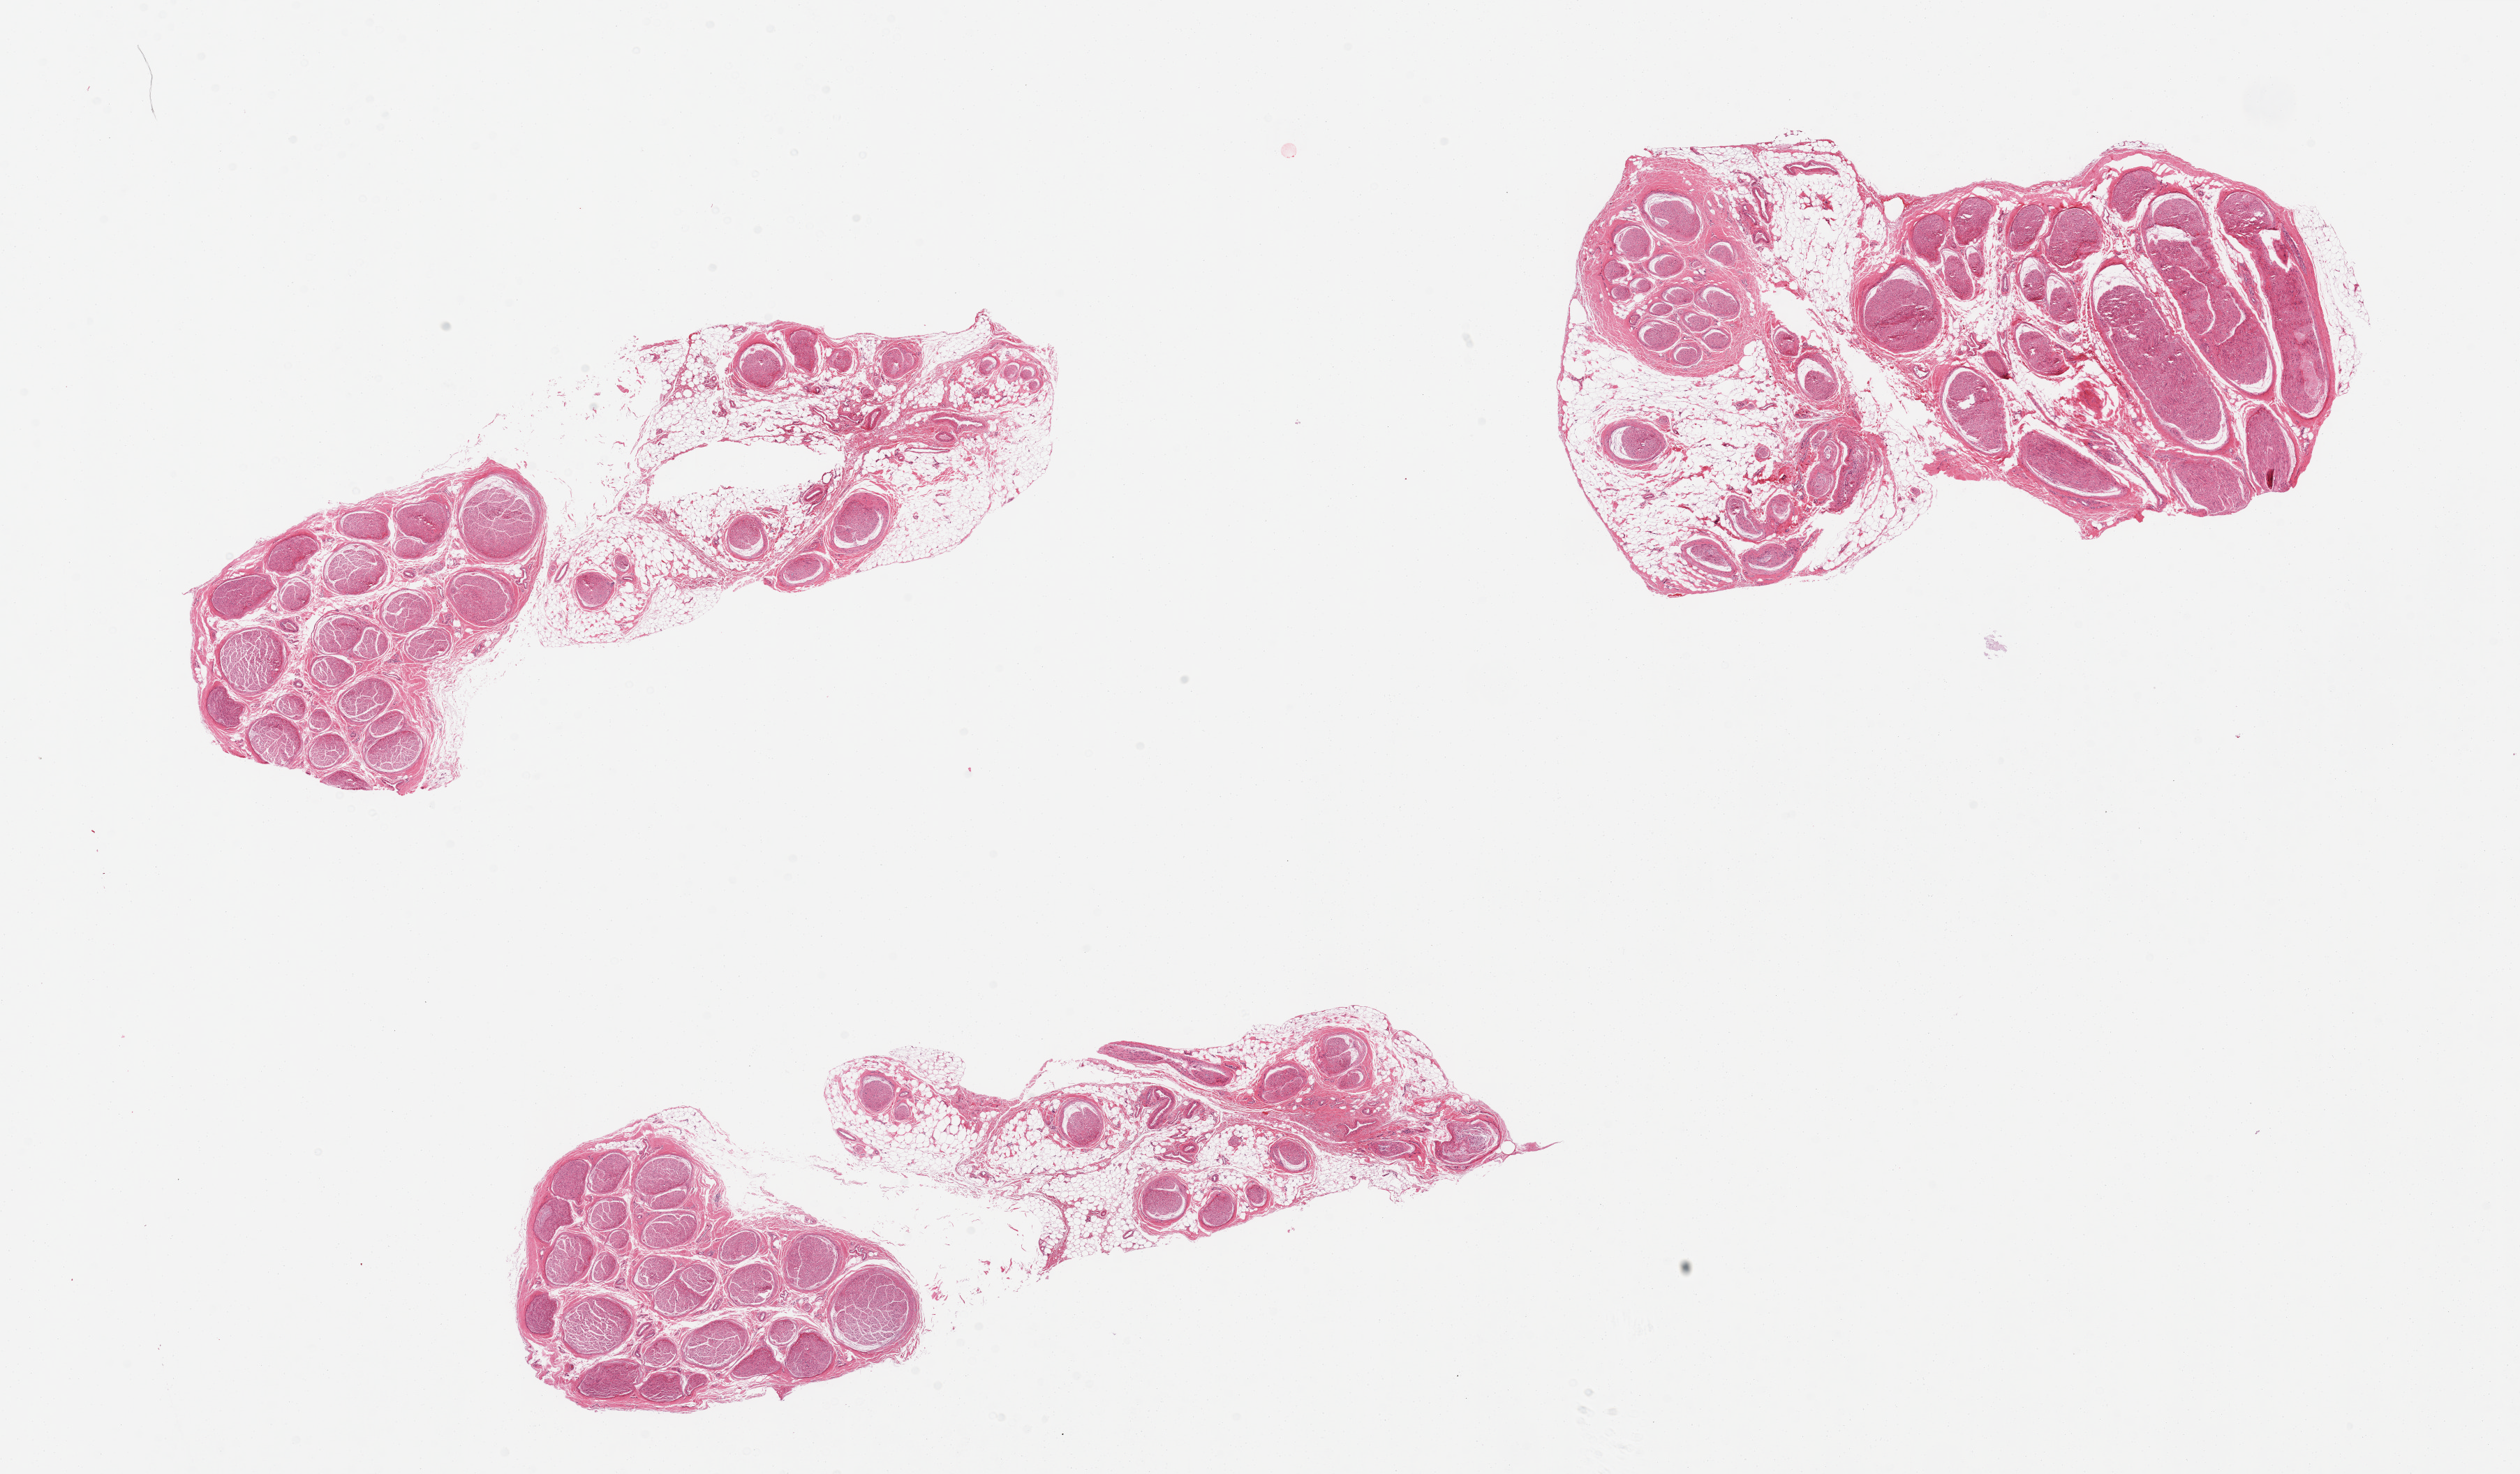
Whole-slide image, hematoxylin and eosin (H&E) stain — a low-resolution overview of the entire scanned area, about 28.5 x 16.7 mm, PAXgene-fixed, paraffin-embedded tissue, sampled site (target tissue): tibial nerve, tissue donor sample. Donor sex: male.
Pathologist's review note for this sample: 3 pieces, each includes about 50% internal and attached fat.